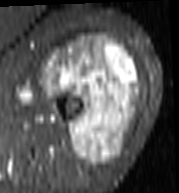
MRI of an extremity soft-tissue mass, one axial slice. Position 66 of 103 along the scan axis. STIR. MR volume resampled by the dataset authors to the PET/CT grid (not the native acquisition matrix). 3.27 mm slice thickness. 179 × 193 image matrix. Female patient. From the clinical record (not read from this slice): histological type: undifferentiated – high grade; grade: high; site of the primary tumour: left thigh.
Annotated regions visible in this slice (expert contour drawn on MRI and transferred to this co-registered scan by the dataset authors):
- gross tumour volume including surrounding oedema: bounding box <43,35,142,166> (left, top, right, bottom; pixels)
- gross tumour volume (mass): <43,35,140,166>